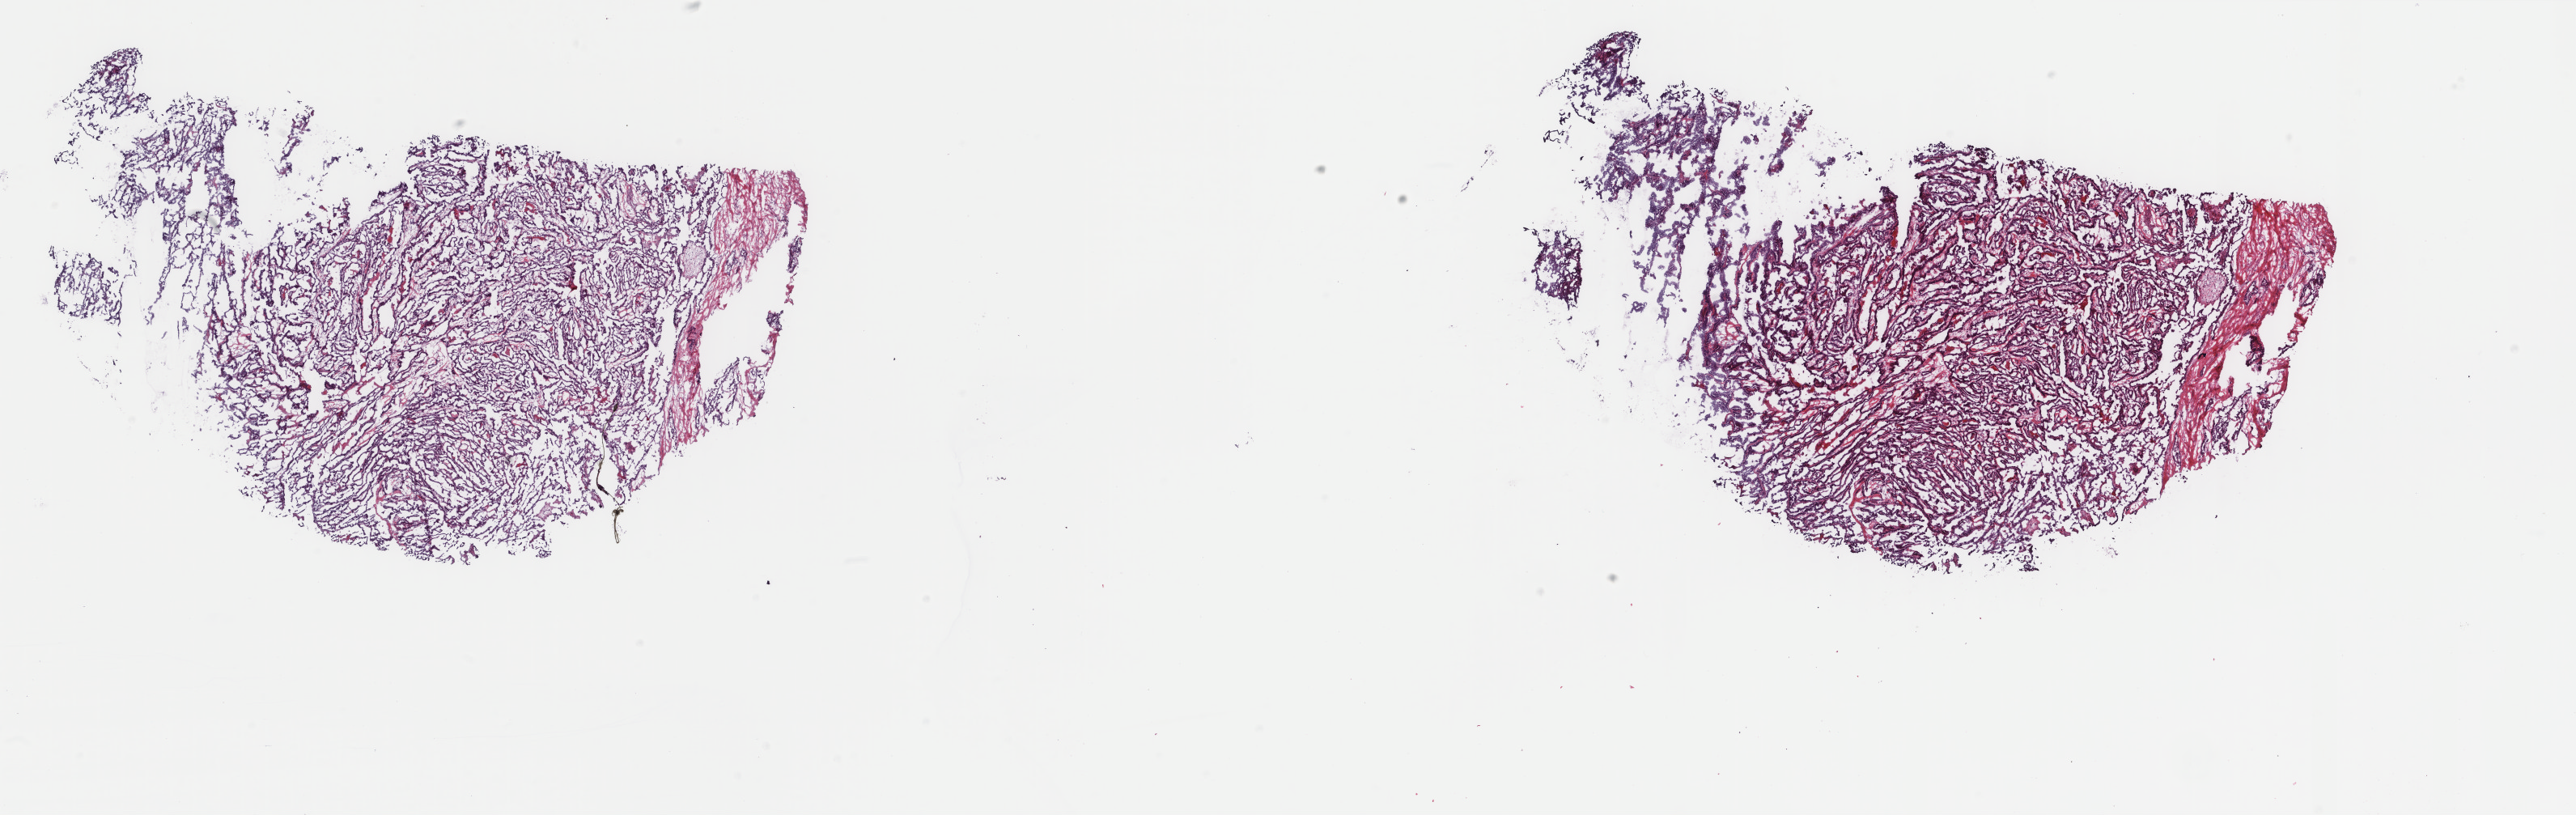
Digitized H&E-stained tissue section (whole slide), whole scanned area (about 25.3 x 8.0 mm, acquisition: 40x scan) shown as a low-resolution overview, frozen section, thyroid, primary tumour sample. Patient: female, age at initial diagnosis 24 years. Pathologist review of this section (percent, as recorded): tumour cells 90%, tumour nuclei 95%, normal cells 0%, stromal cells 10%, necrosis 0%. Inflammatory infiltration, as recorded: lymphocyte infiltration 0%, monocyte infiltration 0%, neutrophil infiltration 0%.
Histologic diagnosis: Papillary adenocarcinoma, NOS. AJCC pathologic stage: I (7th edition). Laterality: left. Lymph nodes positive (case pathology): 5 of 27 examined.